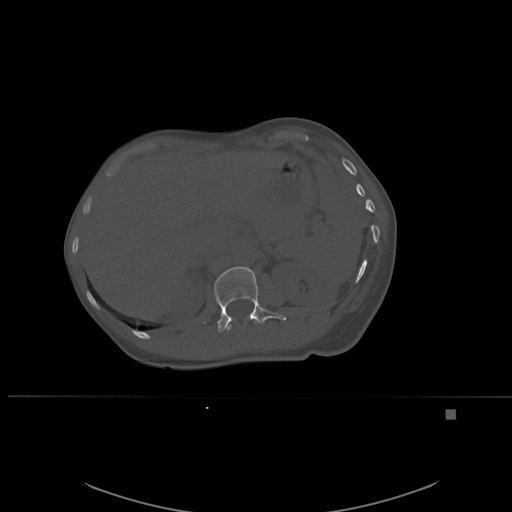
CT including the spine, one axial slice; slice 264 of 537 in the series (ordered by position); bone window (W 1800 / L 400 HU); 512 × 512 image matrix. Female patient, age 45 years. Case-level facts recorded for this patient, not image findings: primary cancer: lung.
Structures marked on this image (semi-automatically segmented with operator editing):
- L1 vertebra: box from (x=204, y=266) to (x=286, y=333) px
- T12 vertebra: (x=225, y=321)–(x=261, y=331)